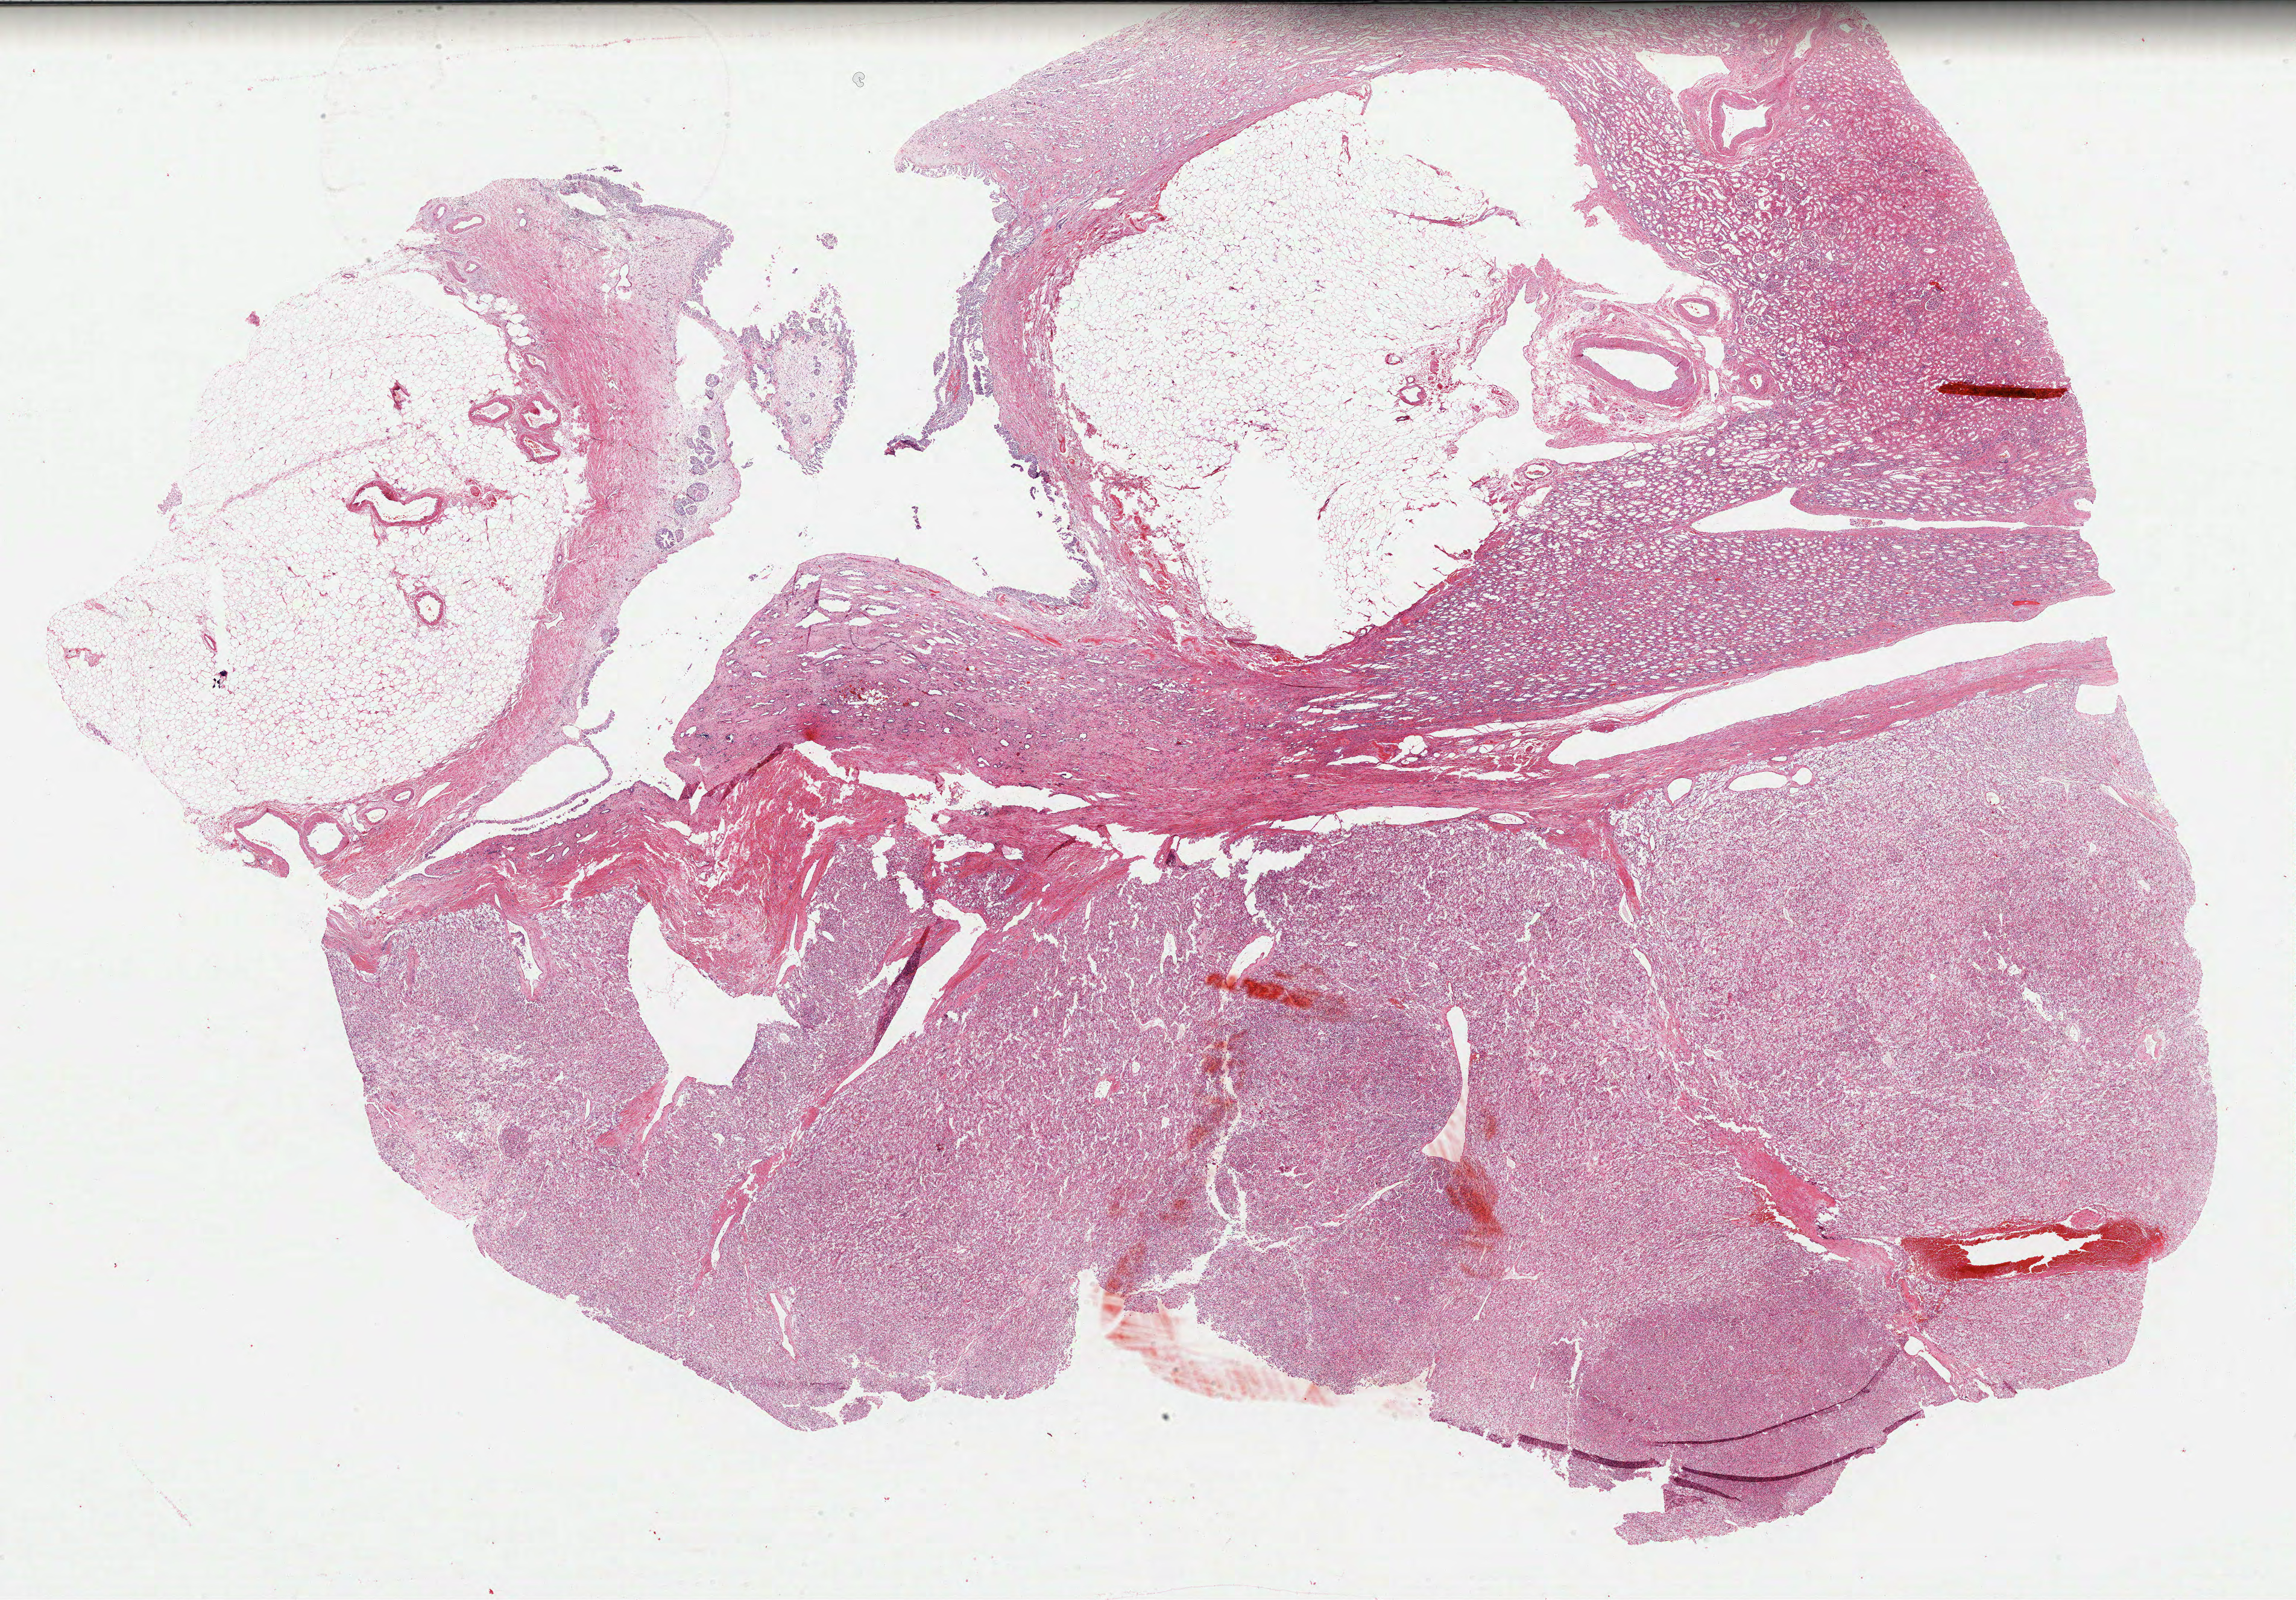
Whole-slide histology image, H&E-stained — low-resolution overview of the scanned area, about 30.7 x 21.4 mm (from a 40x scan); formalin-fixed paraffin-embedded (FFPE) diagnostic section; sample: primary tumour, kidney. Male patient; age at initial diagnosis 74 years. Histologic grade: G3 (poorly differentiated).
* pathologic diagnosis: Clear cell adenocarcinoma, NOS
* AJCC pathologic stage: II (6th edition)
* lymph nodes positive (case pathology): 0 of 13 examined